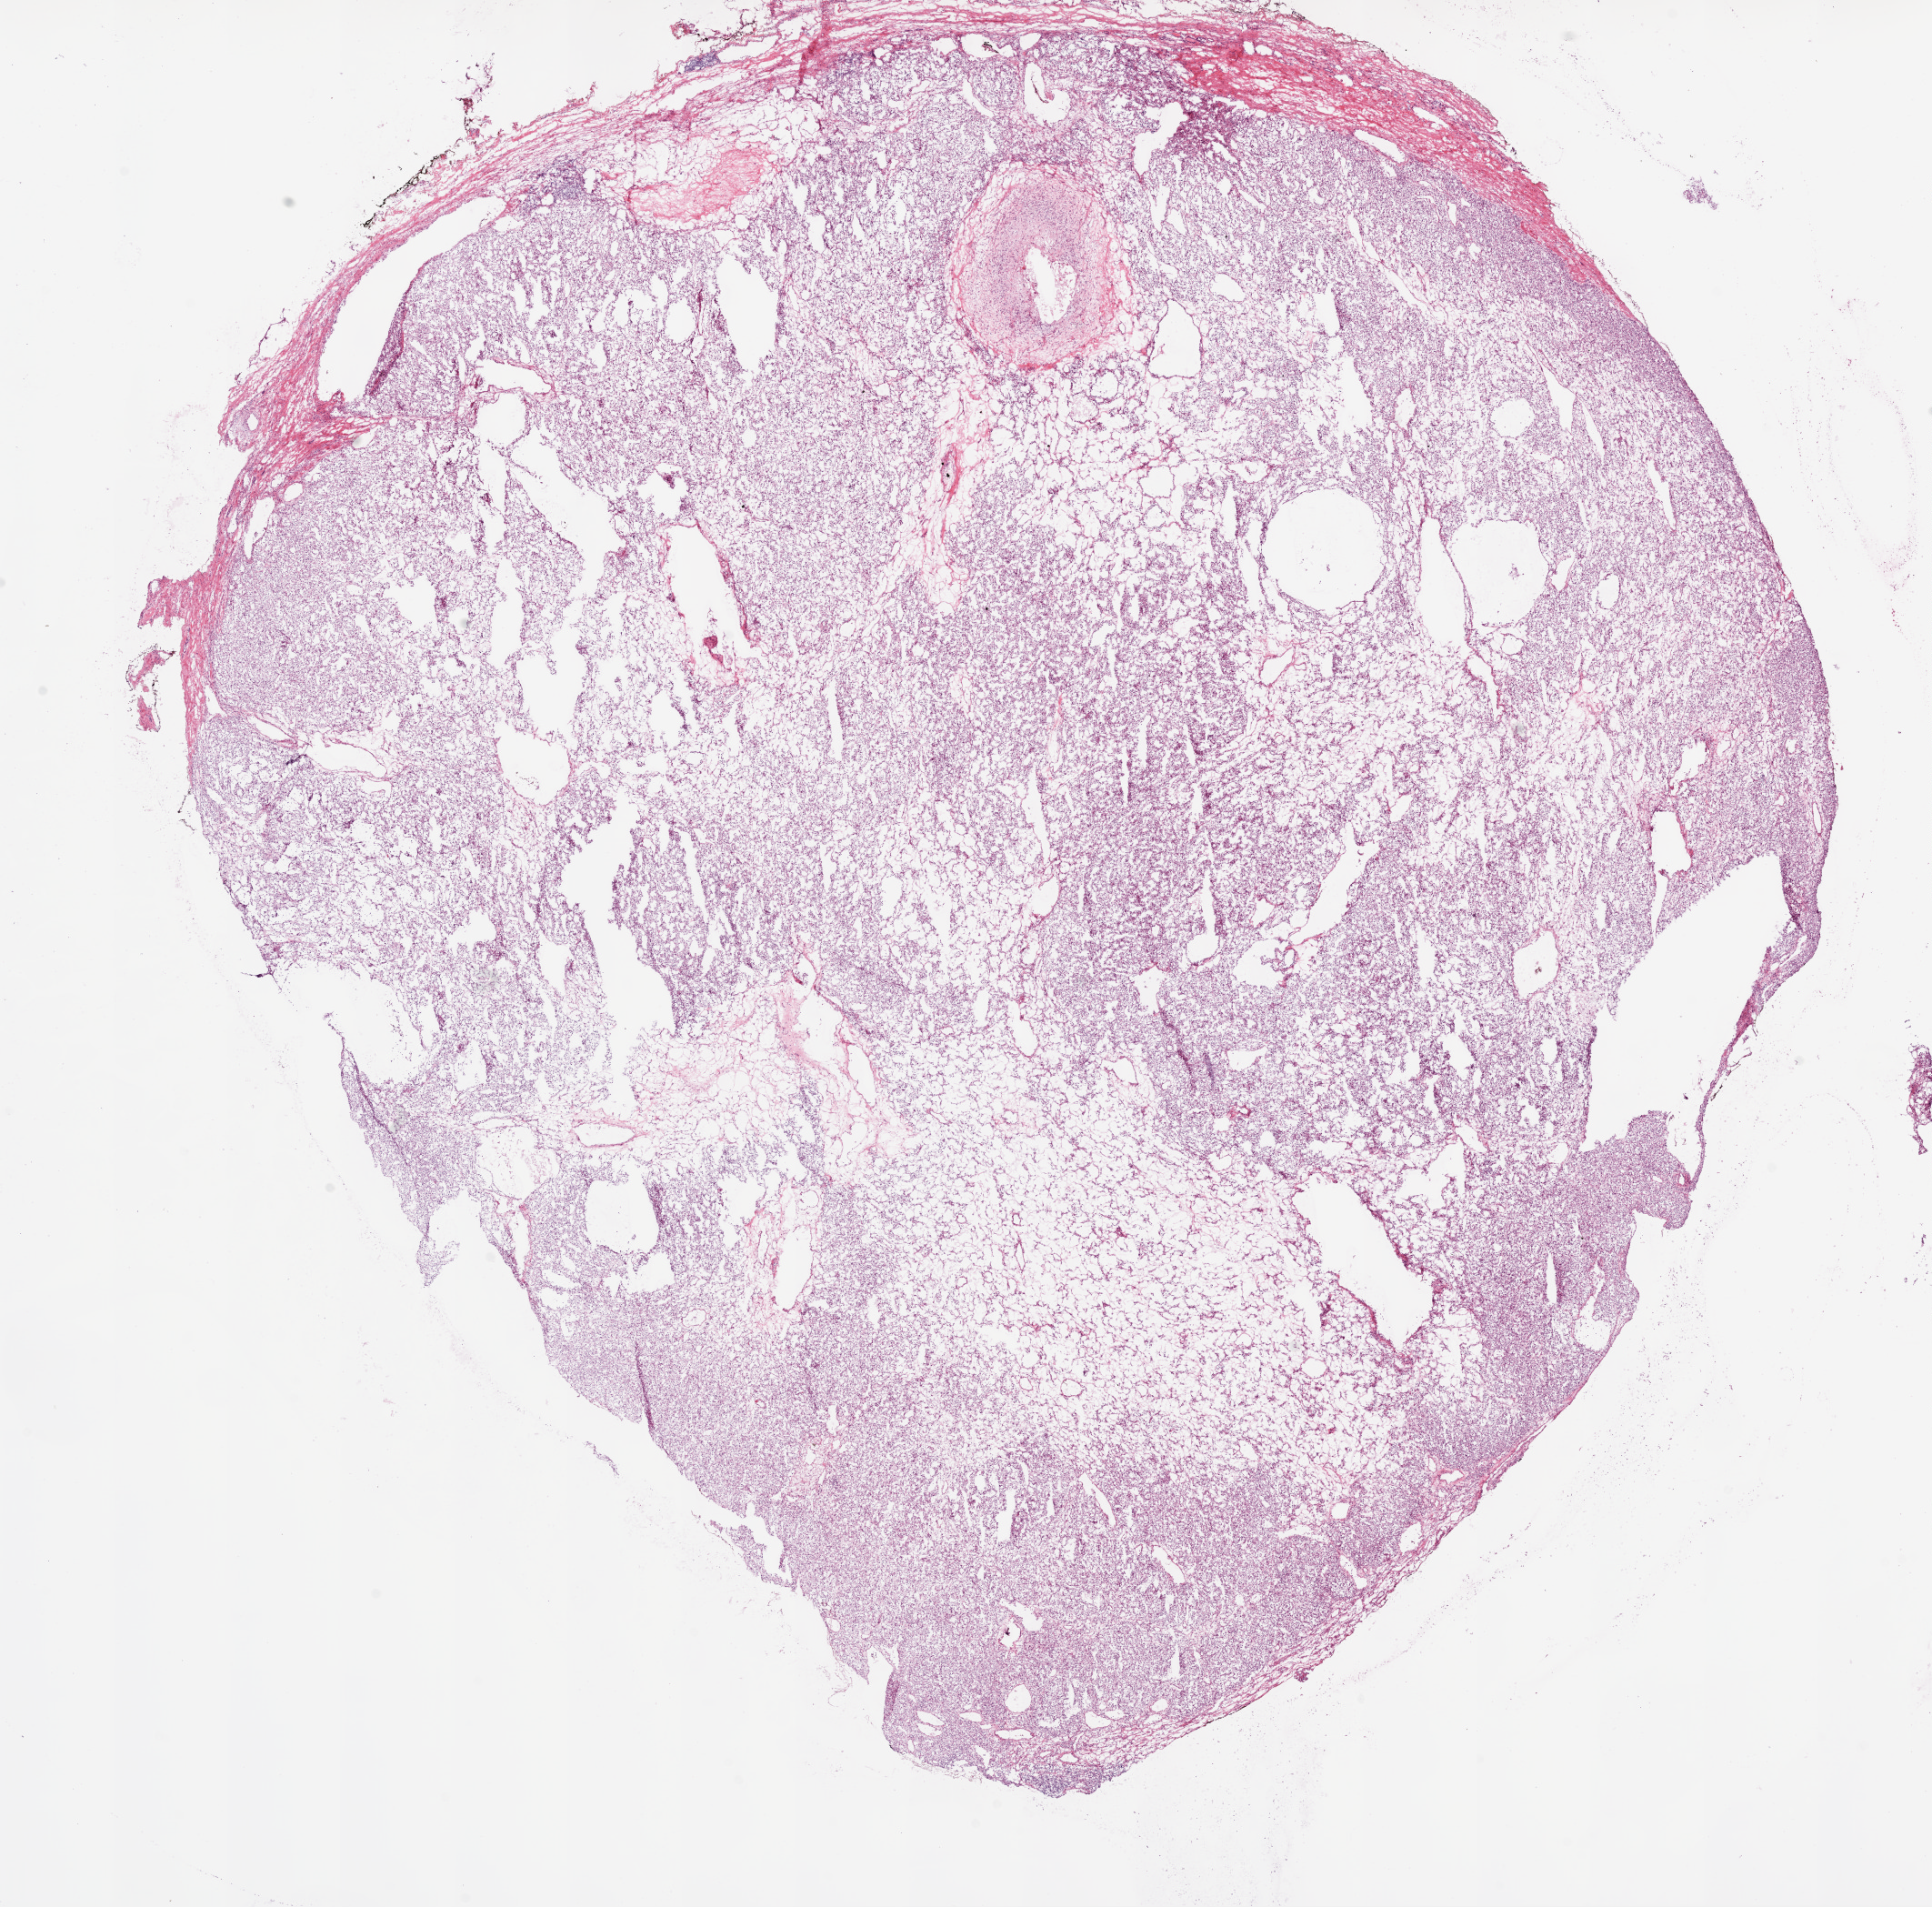
Whole-slide histology image, Hematoxylin and eosin (H&E) stained — whole scanned area (about 17.1 x 16.8 mm, from a 20x scan) shown as a low-resolution overview; frozen section; sample: primary tumour, kidney. Patient: female, age at initial diagnosis 71 years. Histologic grade: G2 (moderately differentiated). Composition of this section per pathologist review: tumour cells 85%, tumour nuclei 80%, normal cells 0%, stromal cells 15%, necrosis 0%.
Histologic diagnosis: Clear cell adenocarcinoma, NOS. AJCC pathologic stage: I (6th edition).